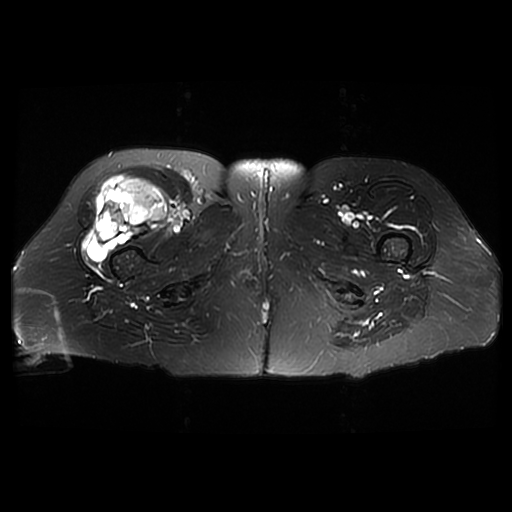
MRI of an extremity soft-tissue mass, one axial slice. Position 30 of 42 along the scan axis. T2-weighted fat-saturated. 6 mm slice thickness. 512 × 512 image matrix, field of view 440 × 440 mm. Female patient. Case-level facts recorded for this patient, not image findings: histological type: pleiomorphic undifferentiated sarcoma; grade: high; site of the primary tumour: right quadricep.
Annotated regions visible in this slice (expert manual segmentation):
- gross tumour volume including surrounding oedema: bounding box [x1, y1, x2, y2] px = [81, 175, 168, 261]
- gross tumour volume (mass): [81, 175, 168, 261]